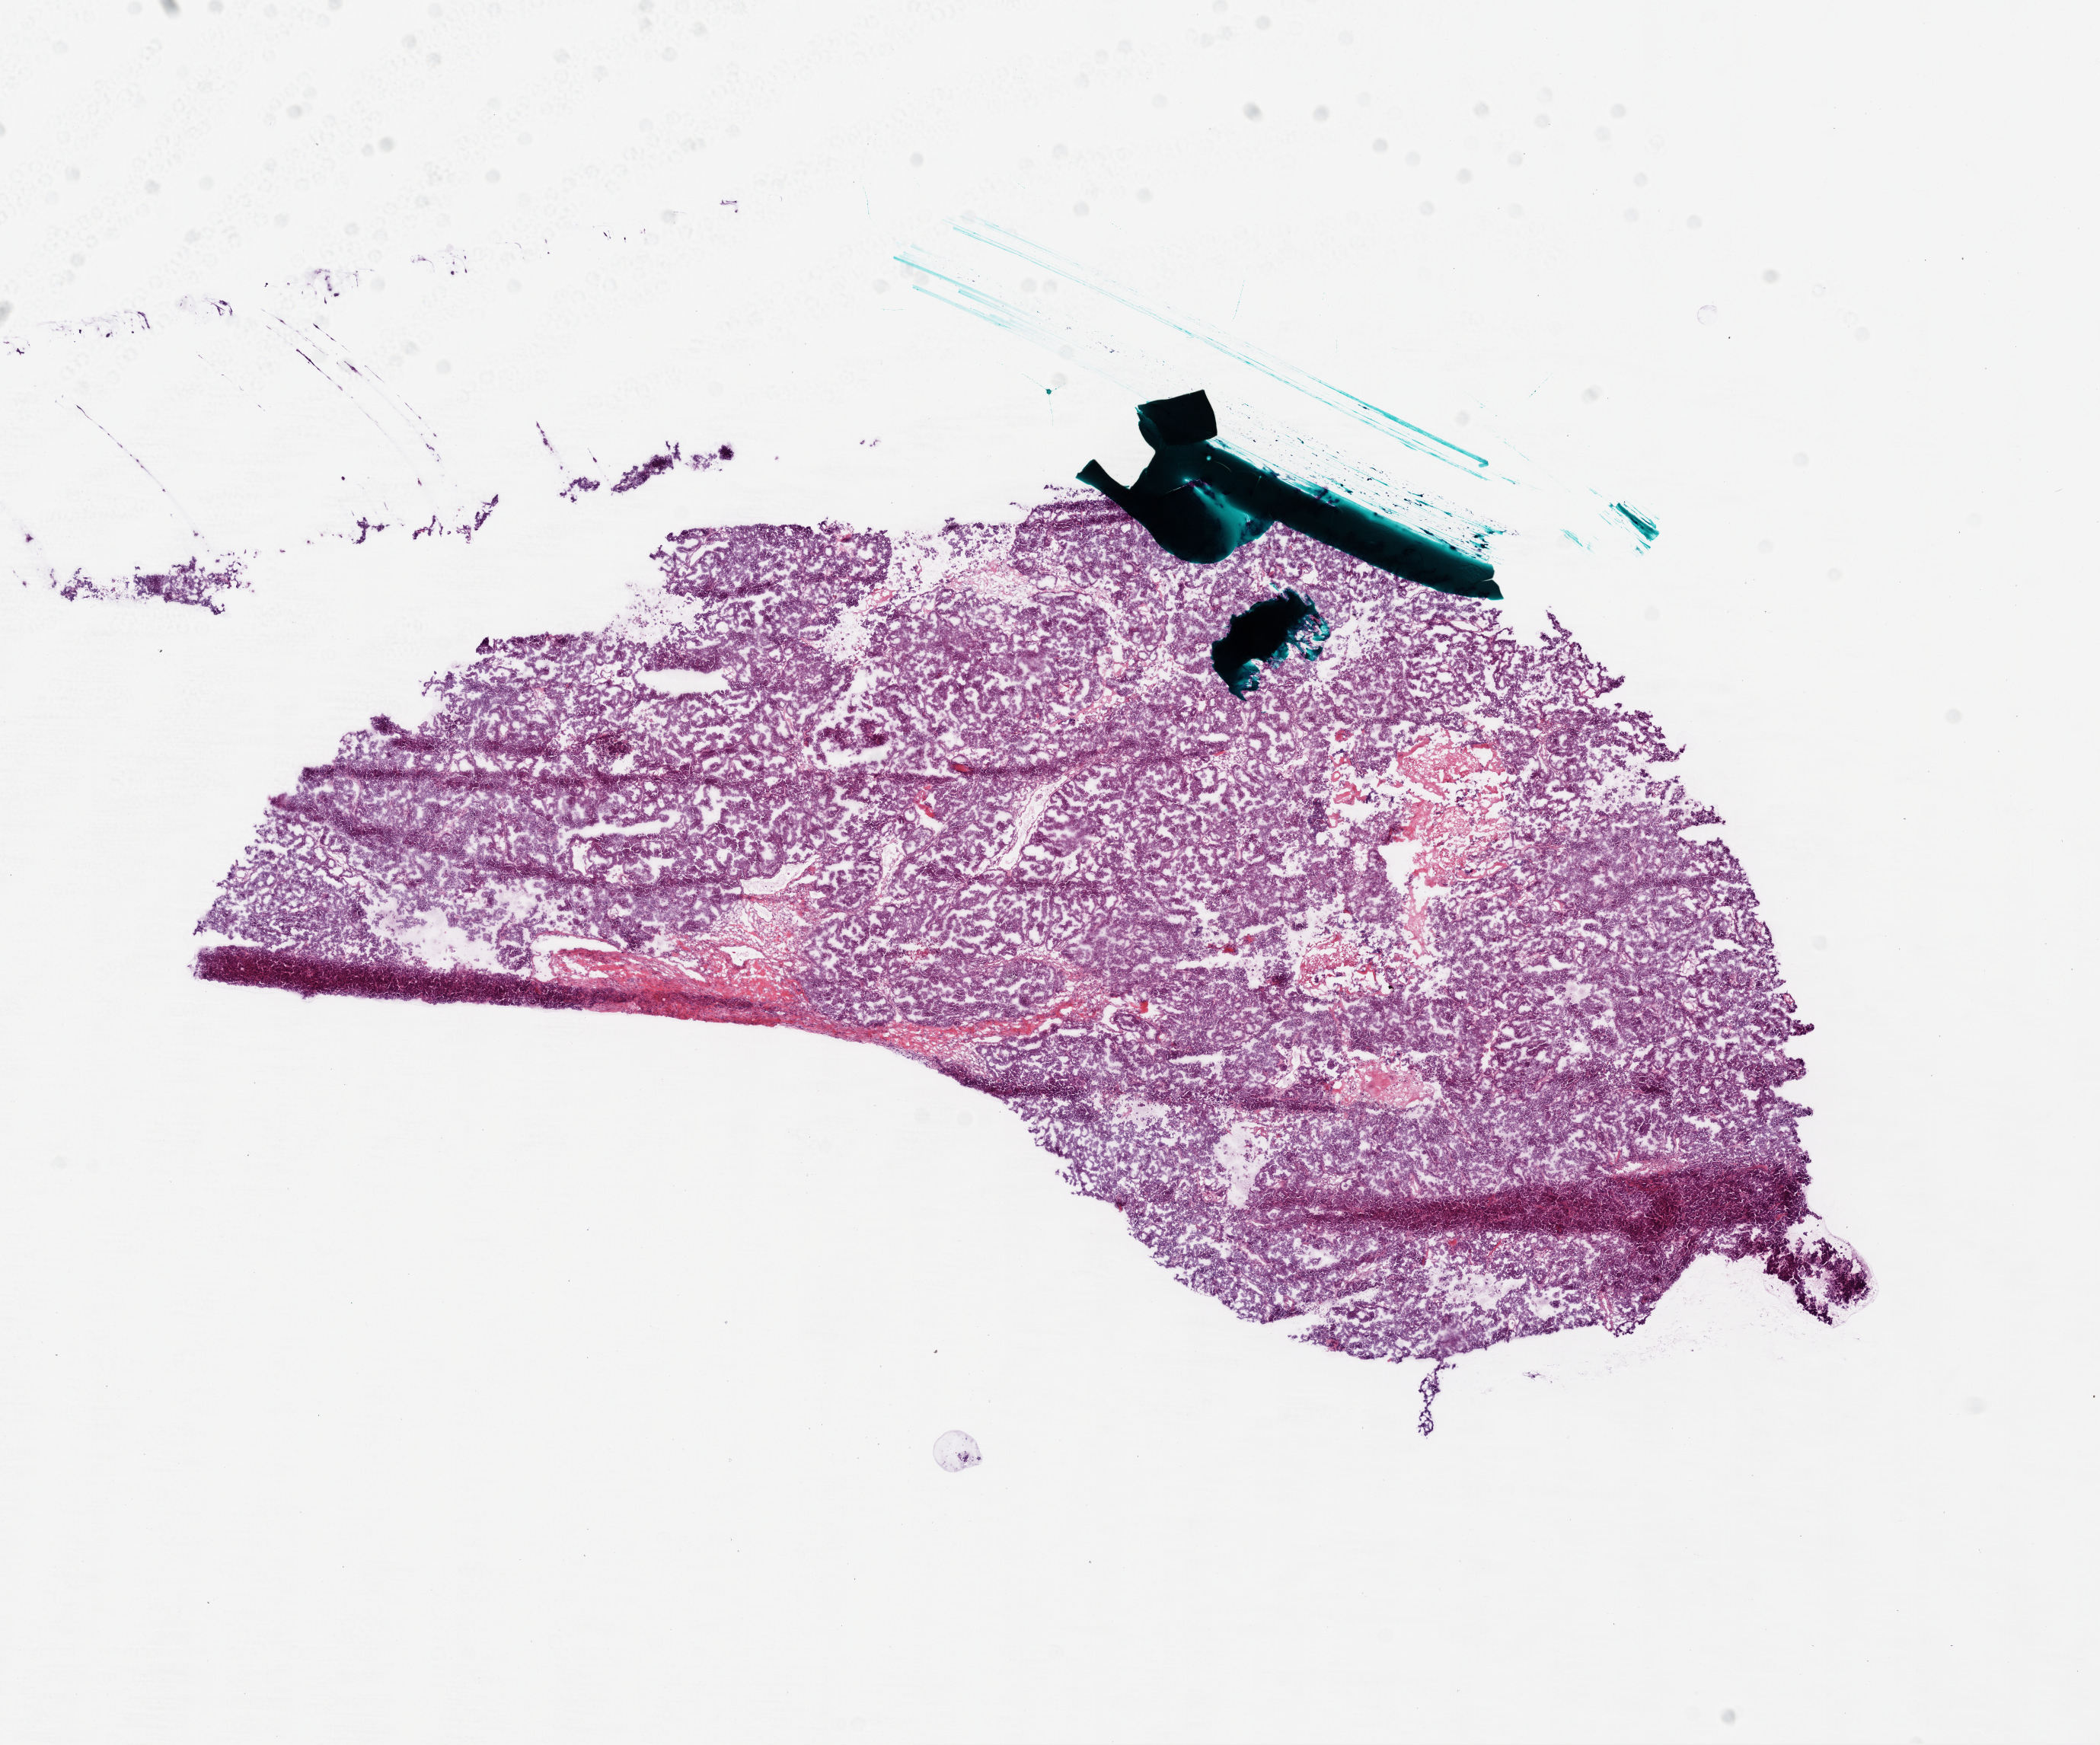
H&E-stained whole-slide image — whole scanned area (about 11.1 x 9.2 mm, acquisition: 20x scan) shown as a low-resolution overview, frozen section, sample: primary tumour, ovary. Patient: female, age at initial diagnosis 68 years.
Diagnosis: Serous cystadenocarcinoma, NOS.